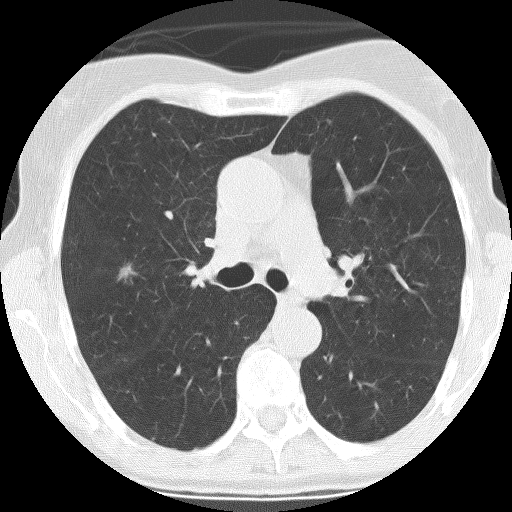
Low-dose screening chest CT, one axial slice. Reconstruction kernel BONE. 120 kVp. Lung window (W 1500 / L -600 HU). 2.5 mm slice thickness. 512 × 512 image matrix, field of view 270 × 270 mm.
Annotated regions visible in this slice (expert manual segmentation):
- lesion 1 (tumor, upper lobe of right lung): box from (x=119, y=265) to (x=133, y=280) px